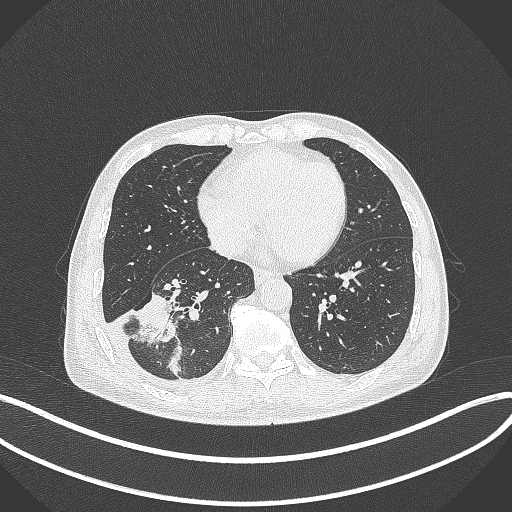
Chest CT, one axial slice. Position 136 of 388 along the scan axis. Reconstruction kernel B70f. 120 kVp. Lung window (W 1500 / L -600 HU). 1 mm slice thickness. 512 × 512 image matrix, field of view 400 × 400 mm. Male patient, age 64 years. From the clinical record (not read from this slice): clinical TNM (as recorded): T3 N0 M0; histopathological grade: G2-3.
Annotated regions visible in this slice (rectangle marked by the reading radiologist):
- lung tumour (recorded histology: adenocarcinoma): bounding box <134,289,180,346> (left, top, right, bottom; pixels)